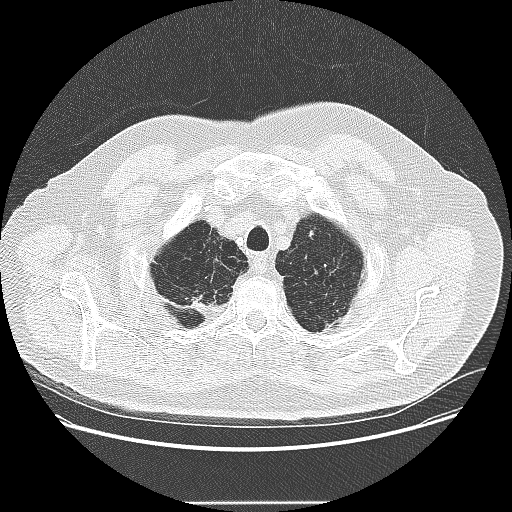
Low-dose screening chest CT, one axial slice; position 220 of 265 along the scan axis; lung window (W 1500 / L -600 HU); 2.5 mm slice thickness; 512 × 512 image matrix, field of view 400 × 400 mm.
Structures marked on this image (manually delineated by an expert):
- lesion 1 (tumor, upper lobe of left lung): bounding box <309,231,314,238> (left, top, right, bottom; pixels)